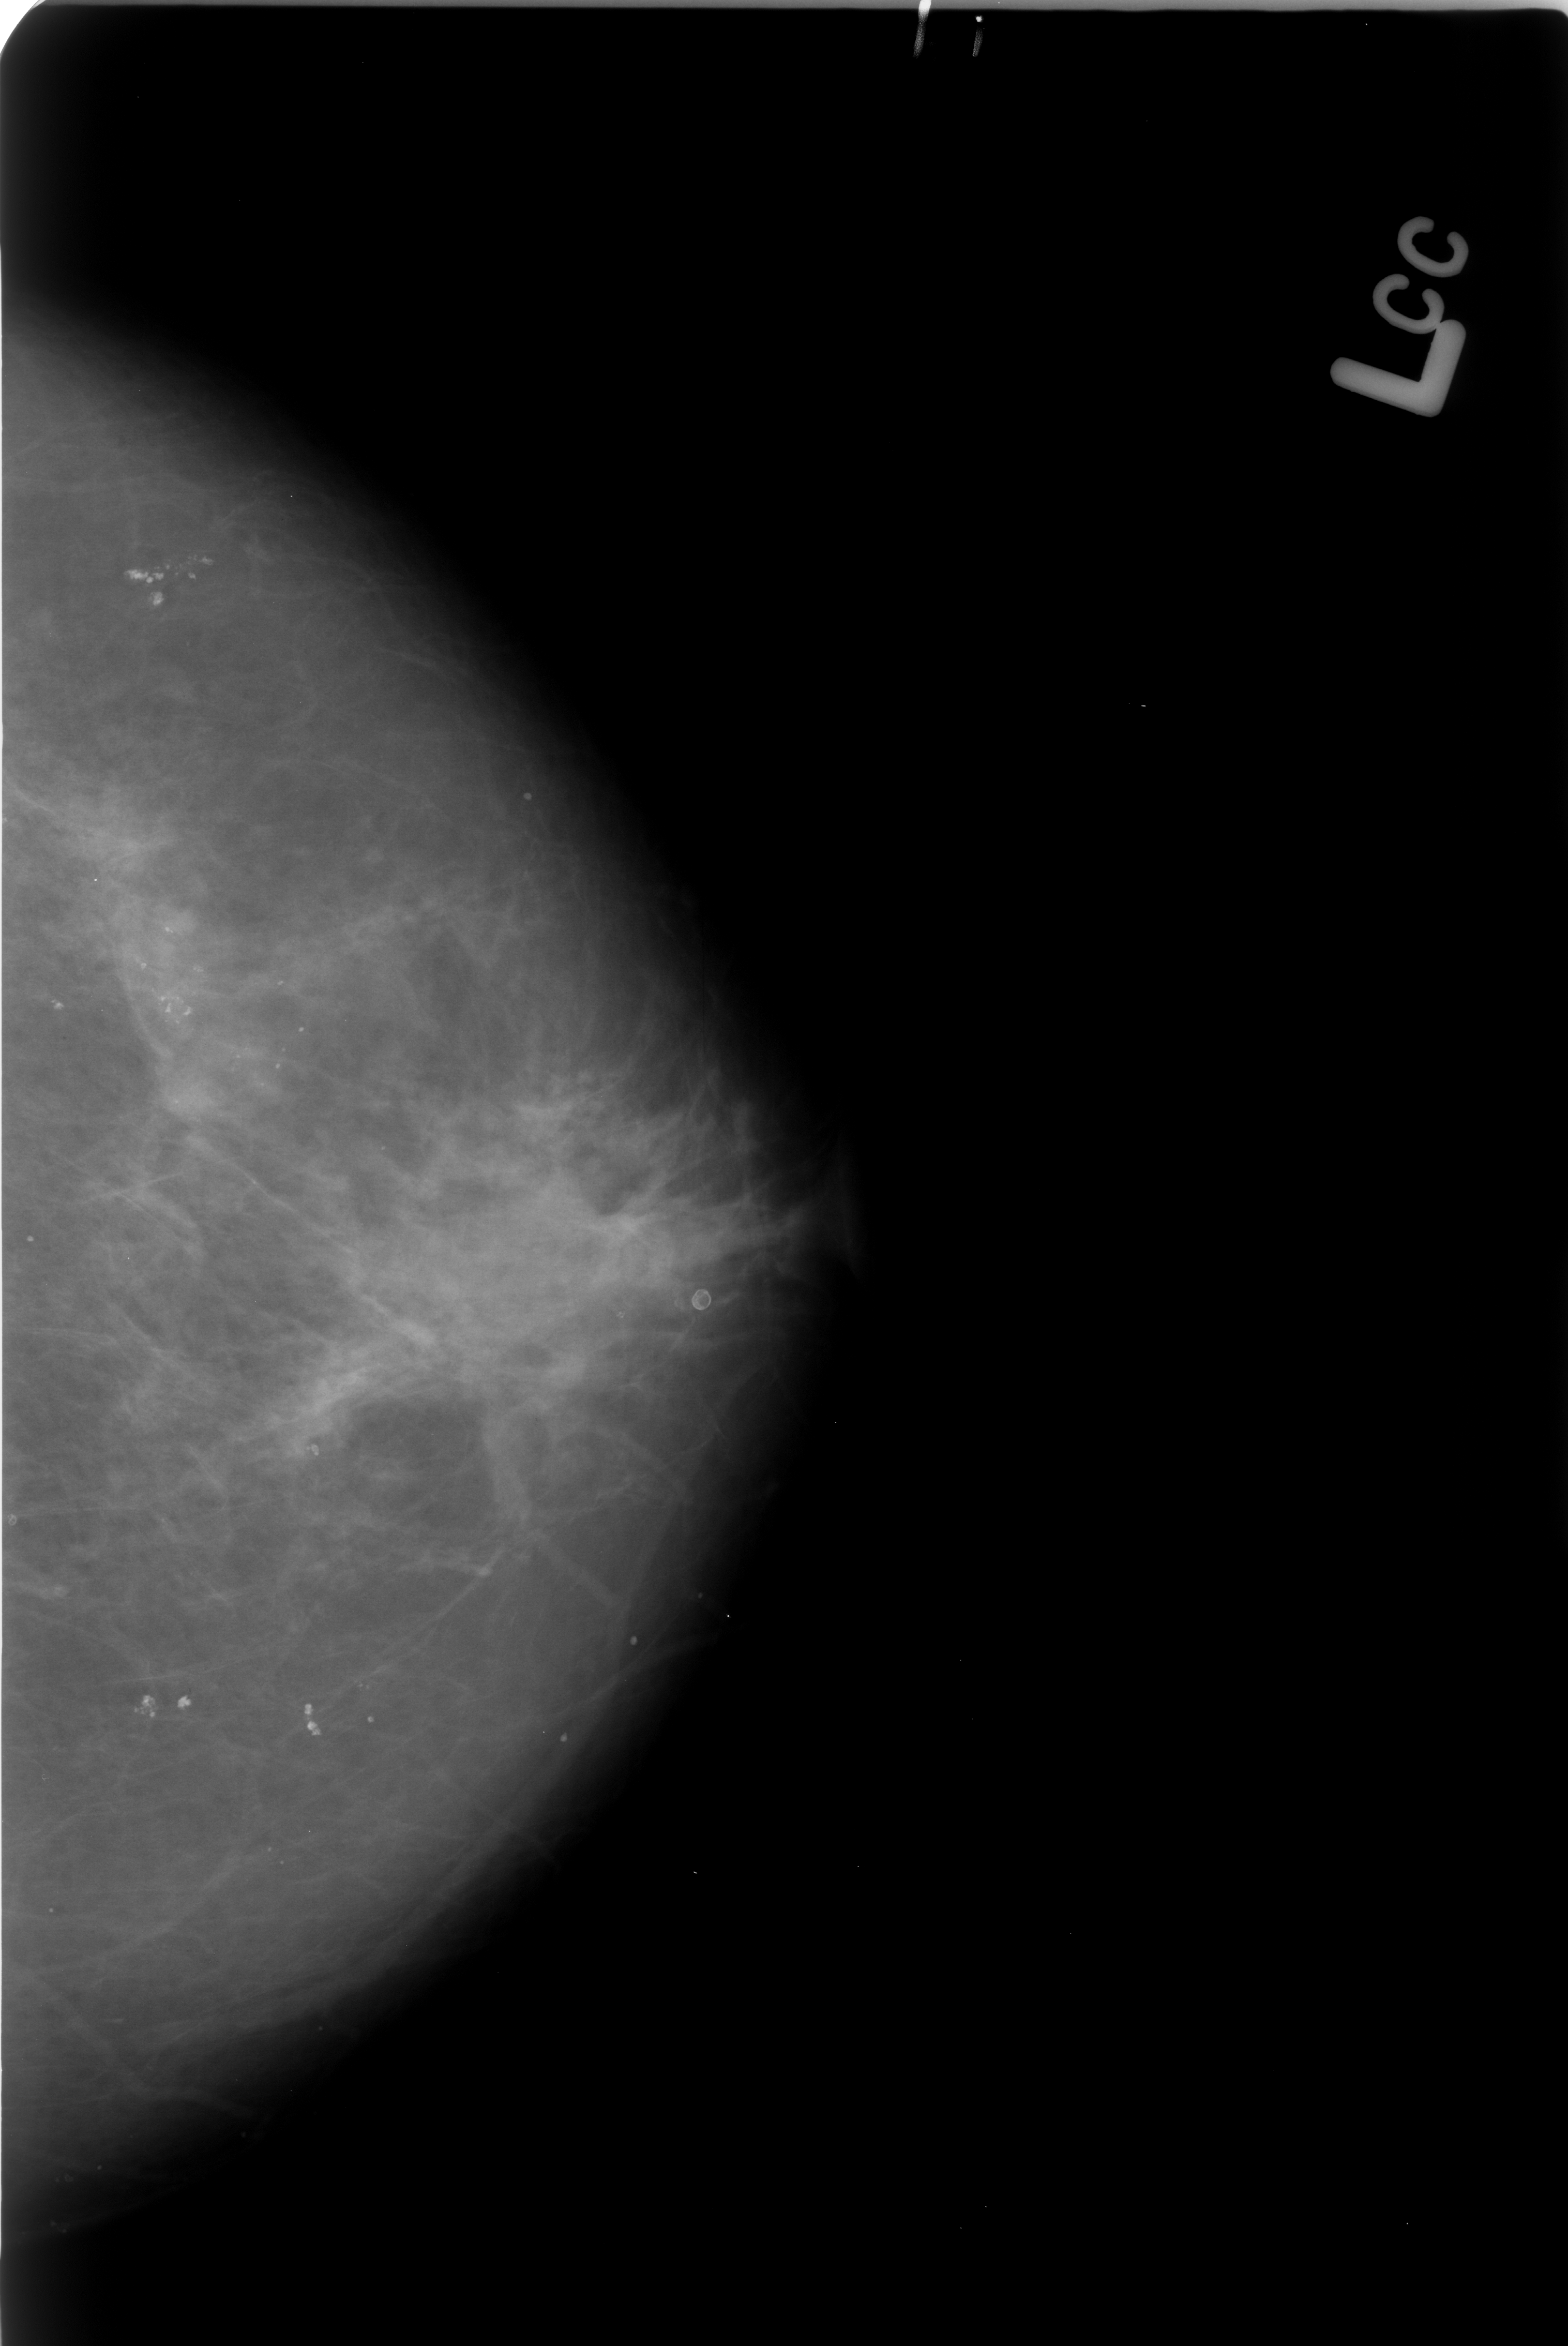
Mammogram (digitized film); left breast; CC view; breast composition: scattered fibroglandular densities (BI-RADS density category 2 of 4); 1568 × 2346 image matrix.
Expert-marked regions of interest on this image (one box per marked abnormality):
- calcifications, morphology pleomorphic, distribution clustered; BI-RADS assessment category 4; pathology (as recorded): benign: bounding box [x1, y1, x2, y2] px = [148, 943, 216, 1052]